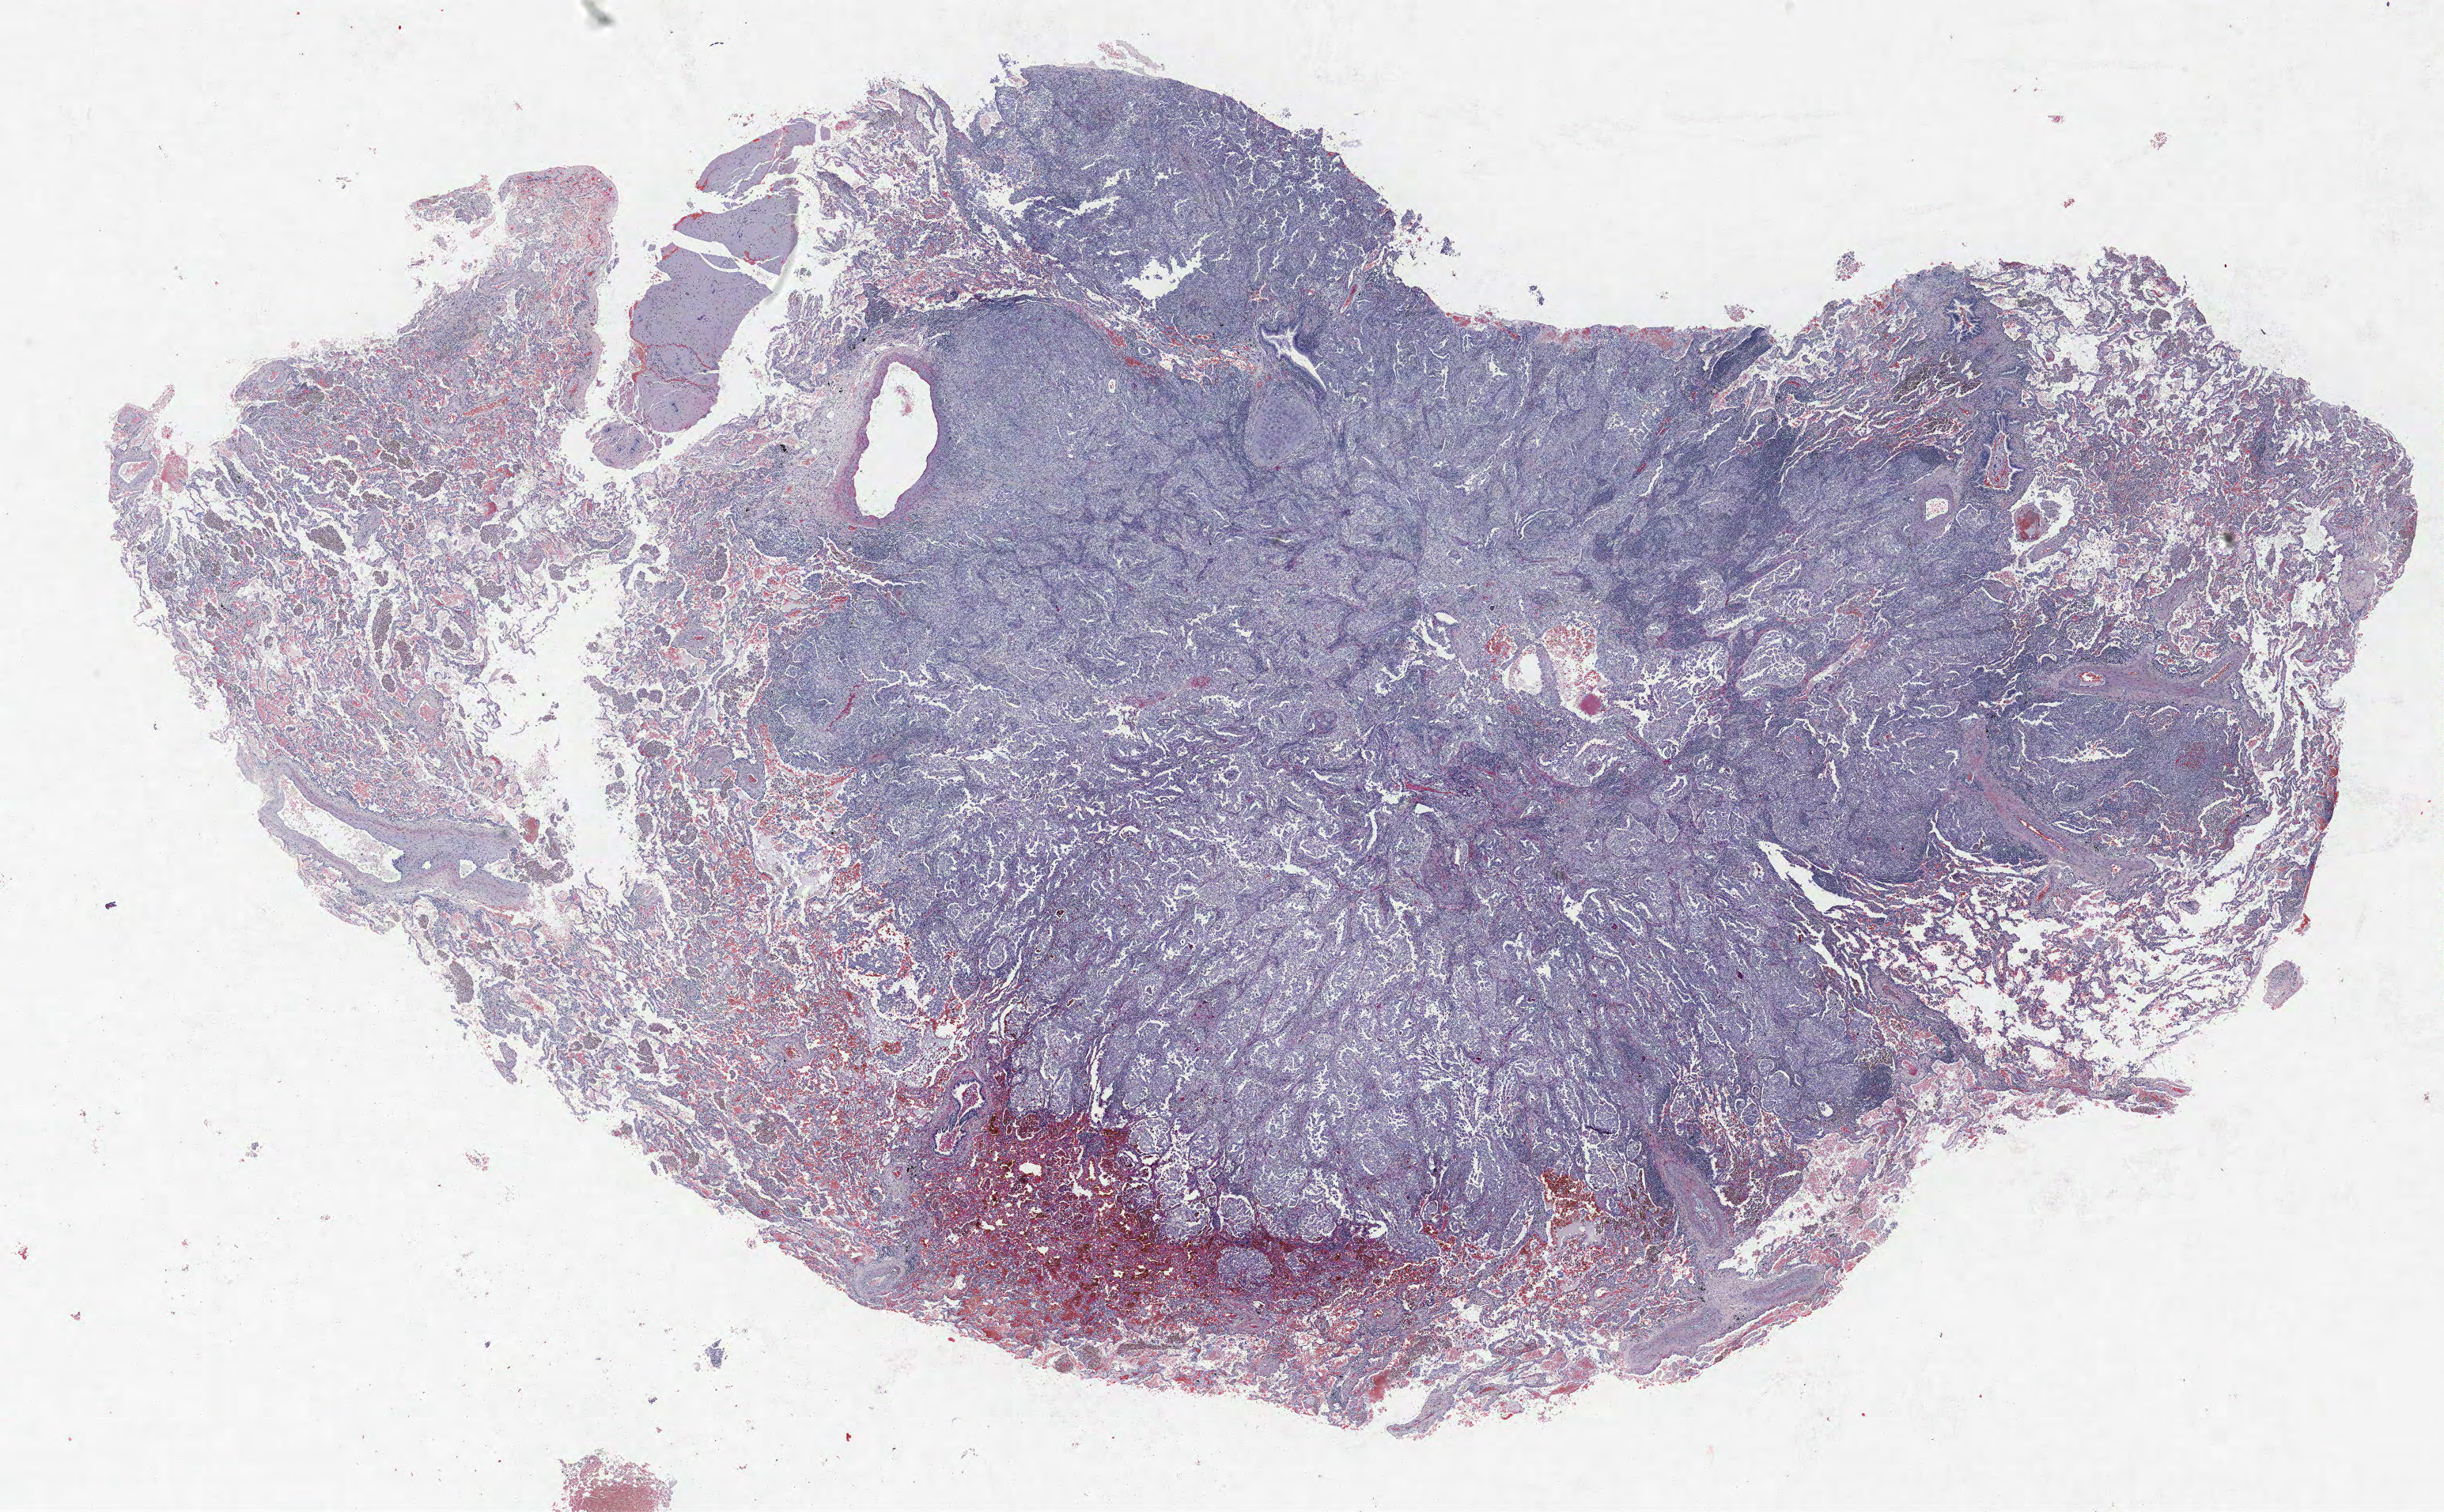
H&E-stained whole-slide image, low-resolution overview of the scanned area, about 24.7 x 15.3 mm (slide scanned at 40x). FFPE section. Lung. Male, age 63 at enrolment. Current smoker at enrolment.
Participant's lung-cancer diagnosis: Adenocarcinoma, NOS.